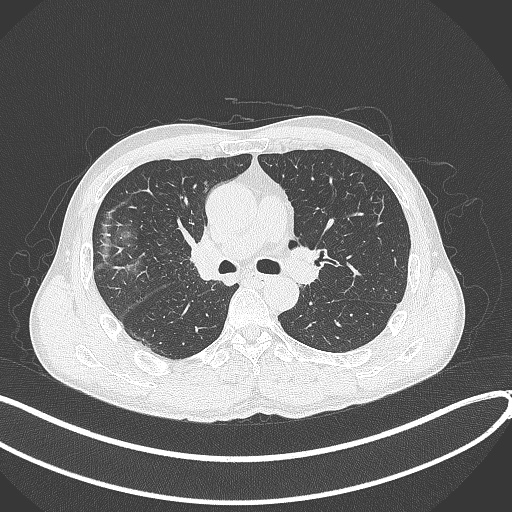
Chest CT, one axial slice; slice 234 of 409 in the series (ordered by position); reconstruction kernel B70f; 120 kVp; lung window (W 1500 / L -600 HU); 1 mm slice thickness; 512 × 512 image matrix, field of view 400 × 400 mm. Male patient, age 53 years. Case-level facts recorded for this patient, not image findings: clinical TNM (as recorded): T1b N0 M0.
Annotated regions visible in this slice (bounding box drawn by a radiologist):
- lung tumour (recorded histology: squamous cell carcinoma): bounding box (x1, y1, x2, y2) in pixels: (181, 226, 229, 291)